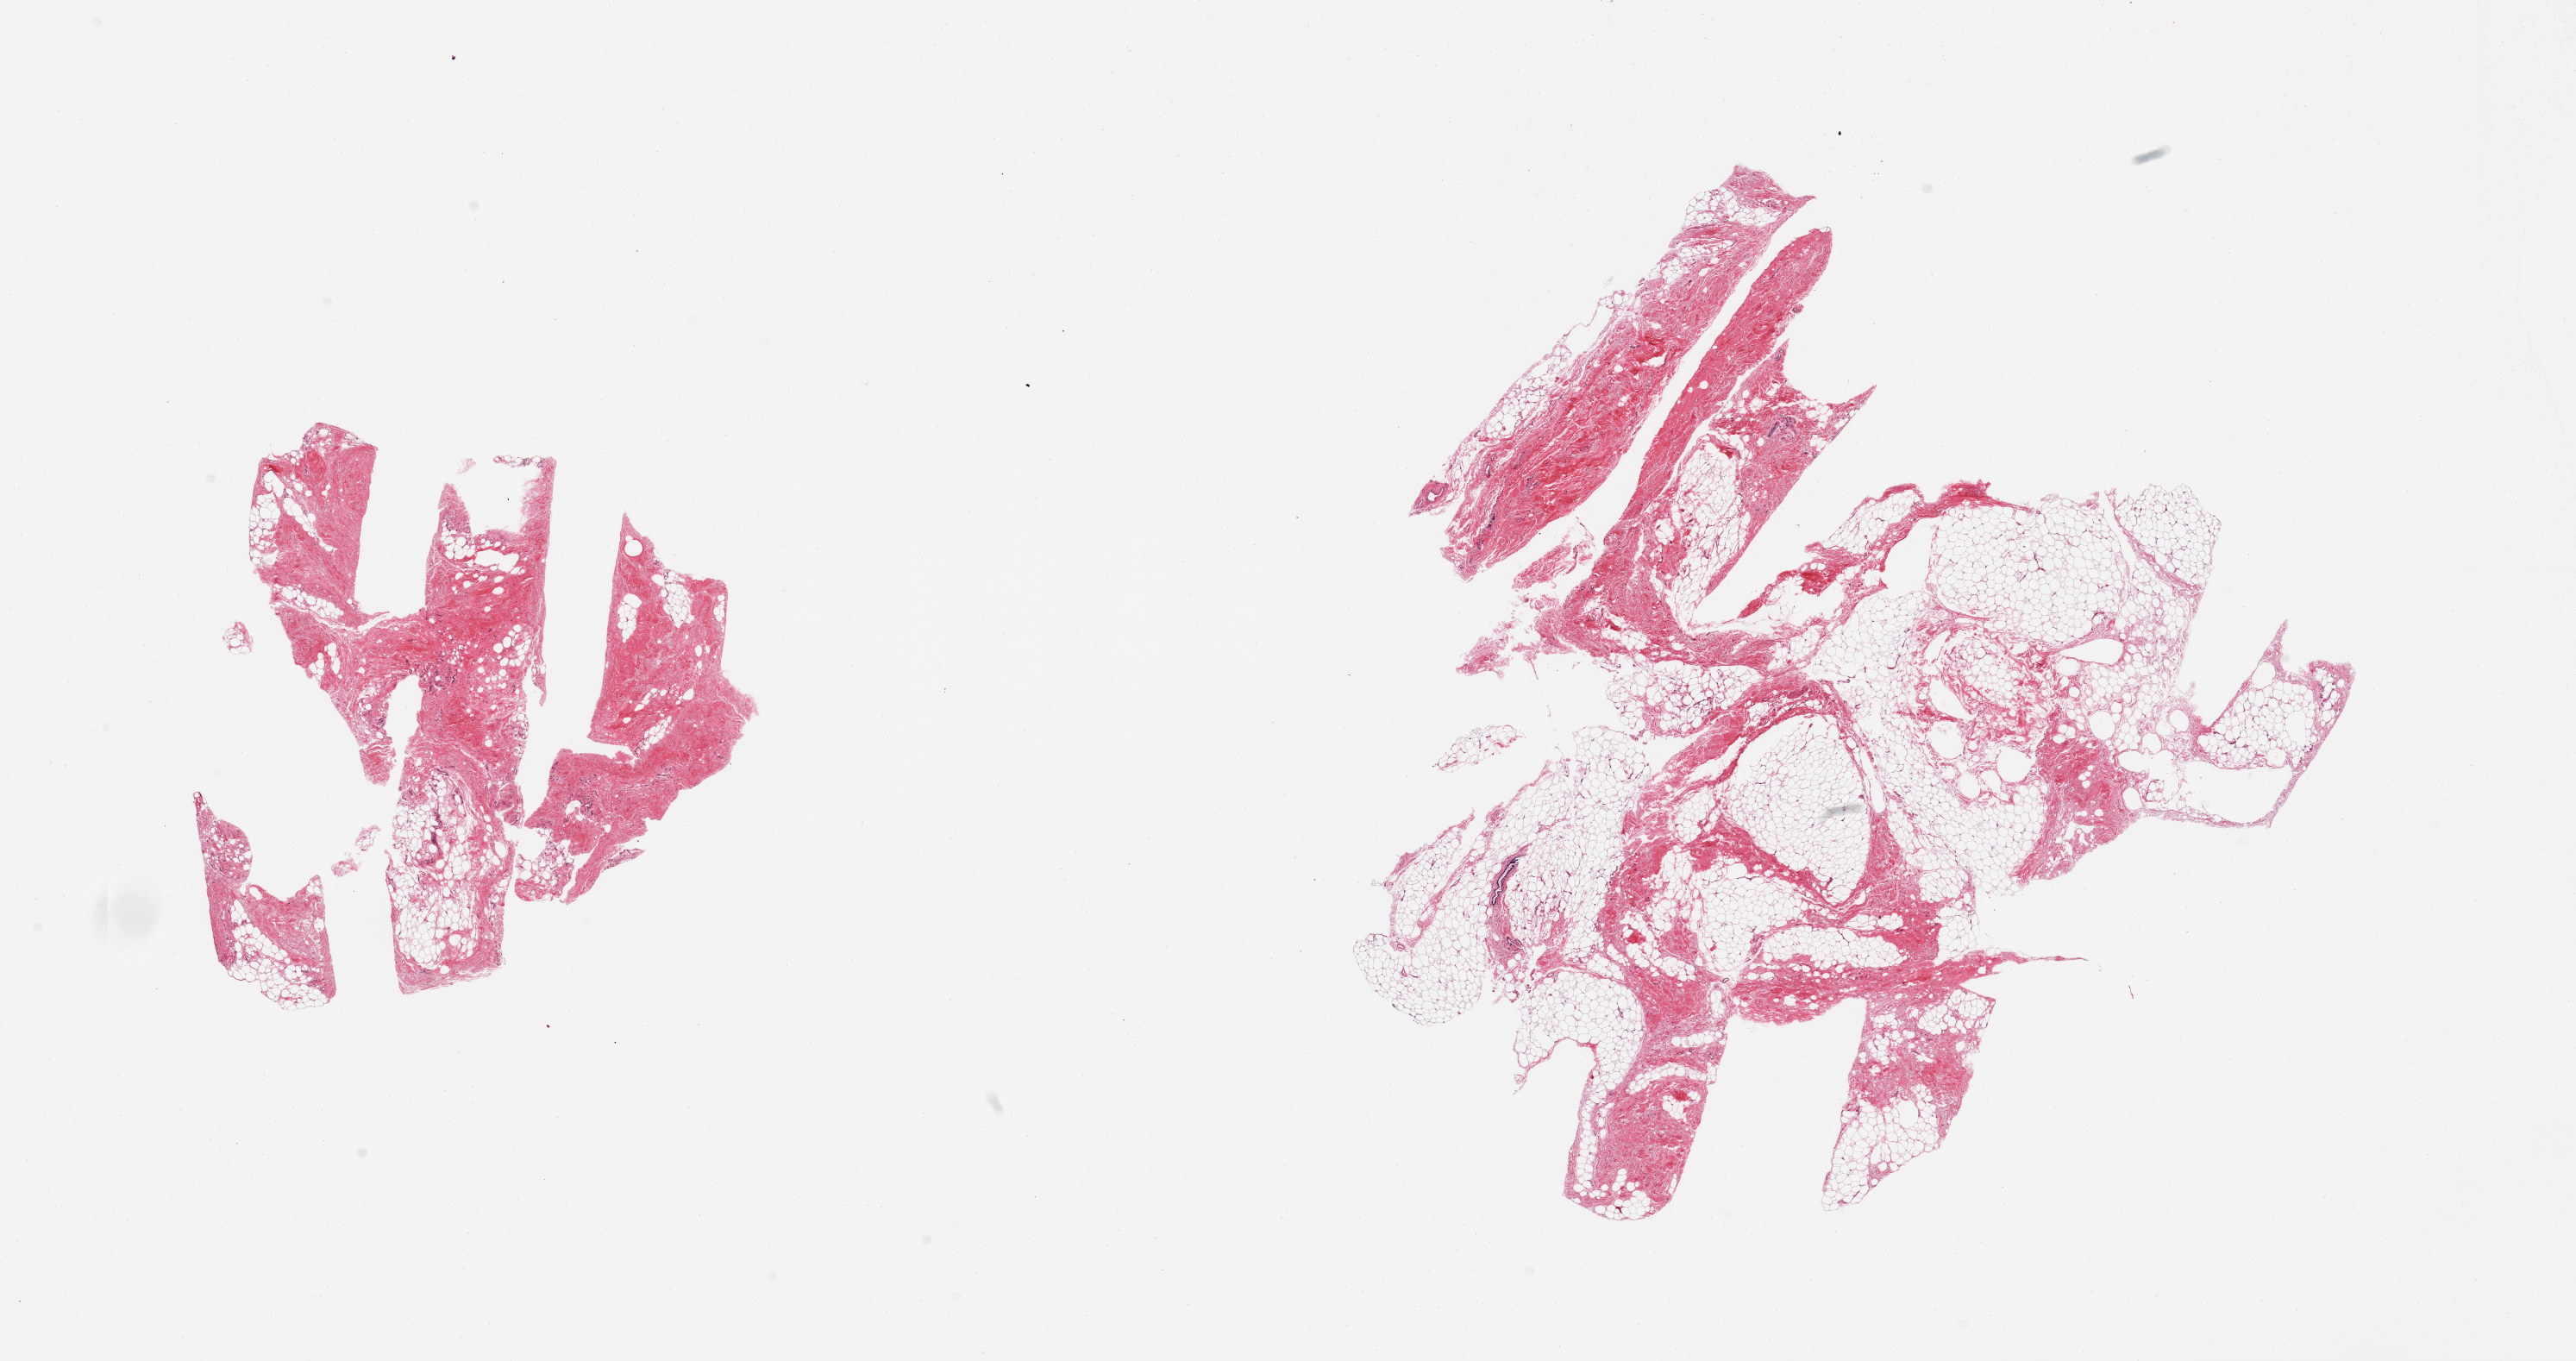
Digitized H&E-stained section, shown as a low-resolution overview of the whole scanned area (about 23.6 x 12.5 mm, from a 20x scan). PAXgene-fixed paraffin-embedded (PFPE) section. Target tissue: breast. Tissue donor sample. Female donor.
- review note (as recorded): 2 pieces; atrophic fibrofatty tissue with rare ducts, no lobules